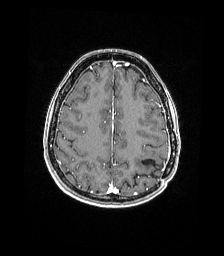
Brain MRI from a brain-tumour surgery series, one axial slice. Slice 55 of 176 in the series (ordered by position). T1-weighted post-contrast. 1 mm slice thickness. 224 × 256 image matrix, field of view 224 × 256 mm. From the clinical record (not read from this slice): histopathology: Atypical meningioma; WHO grade: 2; tumour location: Paramedian Left Parietal.
Structures marked on this image (expert manual segmentation):
- previous resection cavity: bounding box [x1, y1, x2, y2] px = [142, 159, 158, 170]